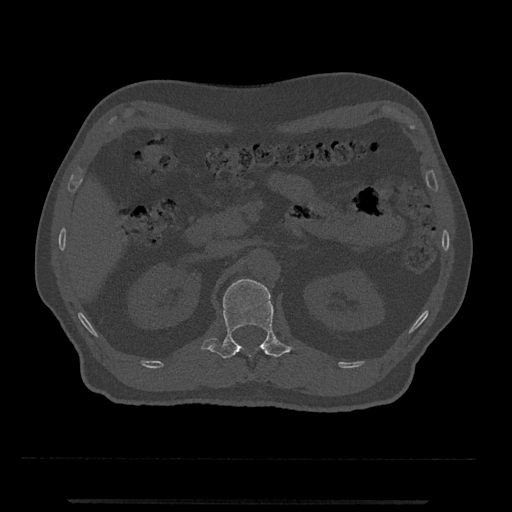
CT including the spine, one axial slice; slice 344 of 797 in the series (ordered by position); reconstruction kernel Br40s/3; bone window (W 1800 / L 400 HU); 0.5 mm slice thickness; 512 × 512 image matrix, field of view 419 × 419 mm. Patient: male, 63 years. Case-level facts recorded for this patient, not image findings: primary cancer: prostate.
Annotated regions visible in this slice (semi-automatic segmentation, software-assisted and operator-edited):
- L1 vertebra: bounding box (x1, y1, x2, y2) in pixels: (201, 279, 294, 359)